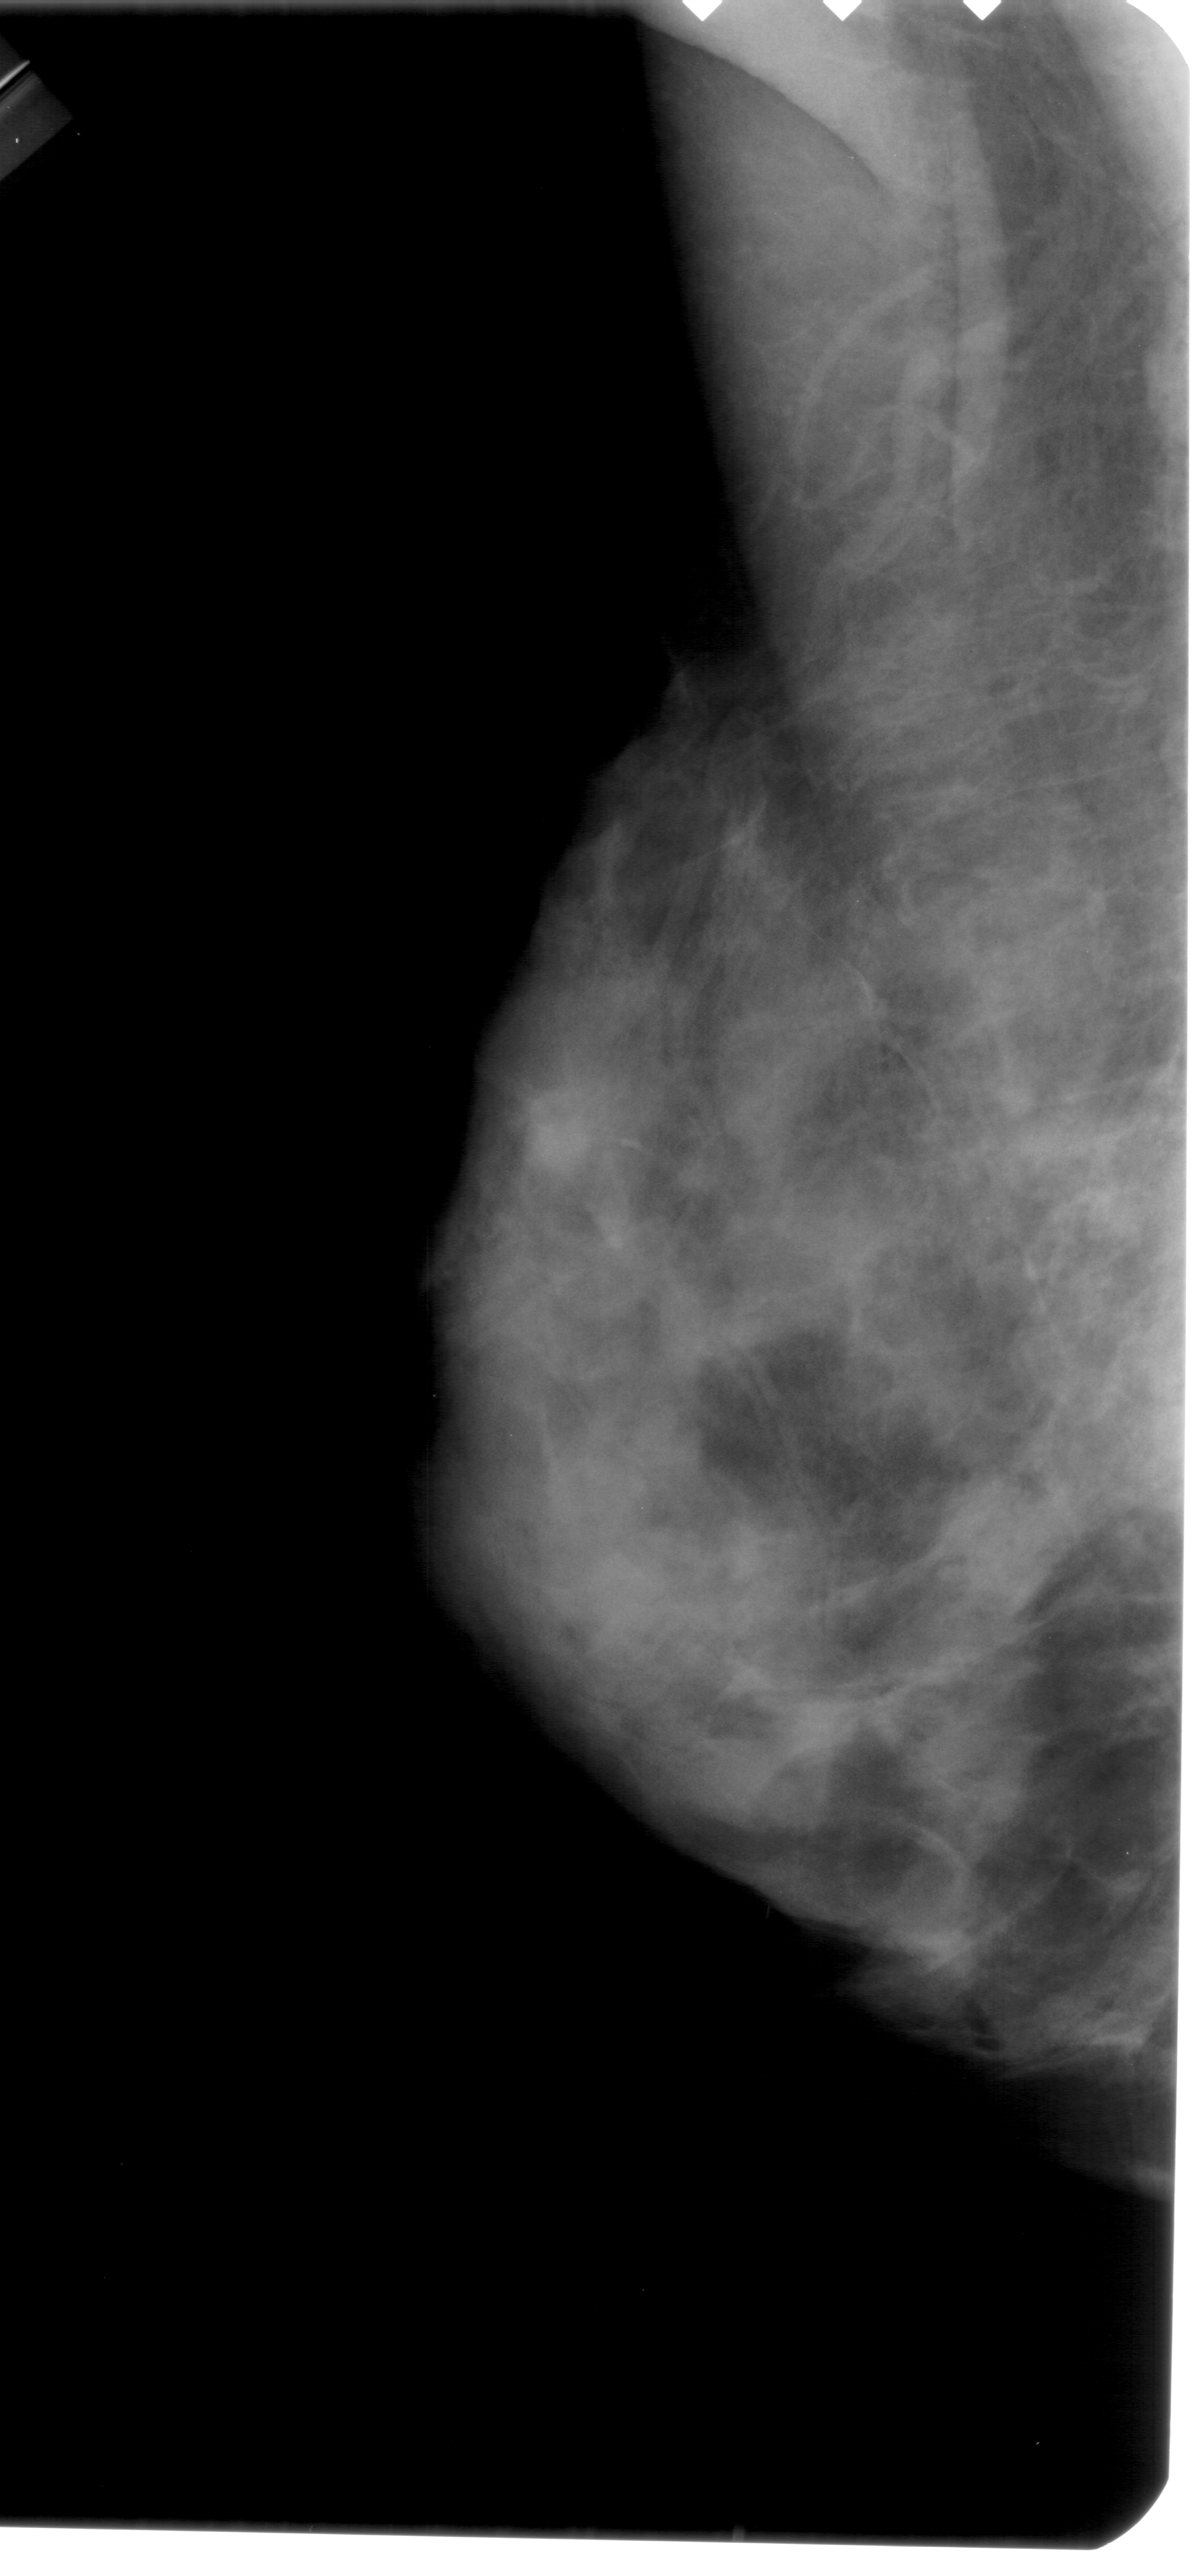
Digitized screen-film mammogram; left breast; MLO view; 1204 × 2576 image matrix.
Expert-marked regions of interest on this film, with their recorded descriptors:
- calcifications, morphology pleomorphic, distribution clustered; BI-RADS assessment category 4; pathology result (as recorded, not read from the image): benign: box from (x=527, y=1105) to (x=596, y=1166) px